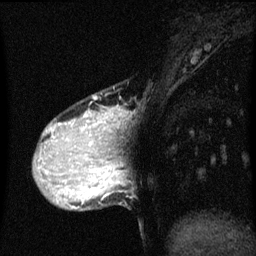
Breast MRI (dynamic contrast-enhanced), one sagittal slice. Position 15 of 60 along the scan axis. Dynamic contrast-enhanced series, image 2 of 3 at this slice position (ordered by acquisition). 1.5 T. TE 4.2 ms, TR 8 ms. 2 mm slice thickness. 256 × 256 image matrix, field of view 200 × 200 mm. Patient: female, 36 years.
Structures marked on this image (semi-automatic segmentation, software-assisted and operator-edited):
- analysis volume of interest (the breast-tissue region the enhancement analysis was run in; not a lesion): bounding box [x1, y1, x2, y2] px = [34, 106, 121, 169]
- tumour enhancement mask (voxels above the 70 % enhancement threshold inside the analysis volume of interest): [44, 108, 120, 169]